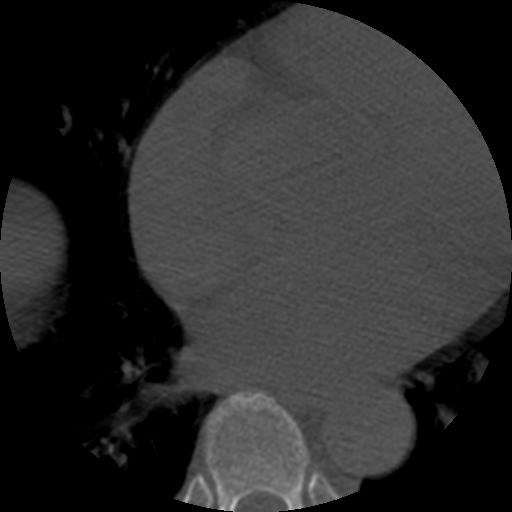
CT including the spine, one axial slice; slice 338 of 508 in the series (ordered by position); bone window (W 1800 / L 400 HU); 512 × 512 image matrix, field of view 160 × 160 mm. Patient age 57 years. From the clinical record (not read from this slice): primary cancer: prostate.
Structures marked on this image (semi-automatically segmented with operator editing):
- T7 vertebra: bounding box <206,394,310,512> (left, top, right, bottom; pixels)